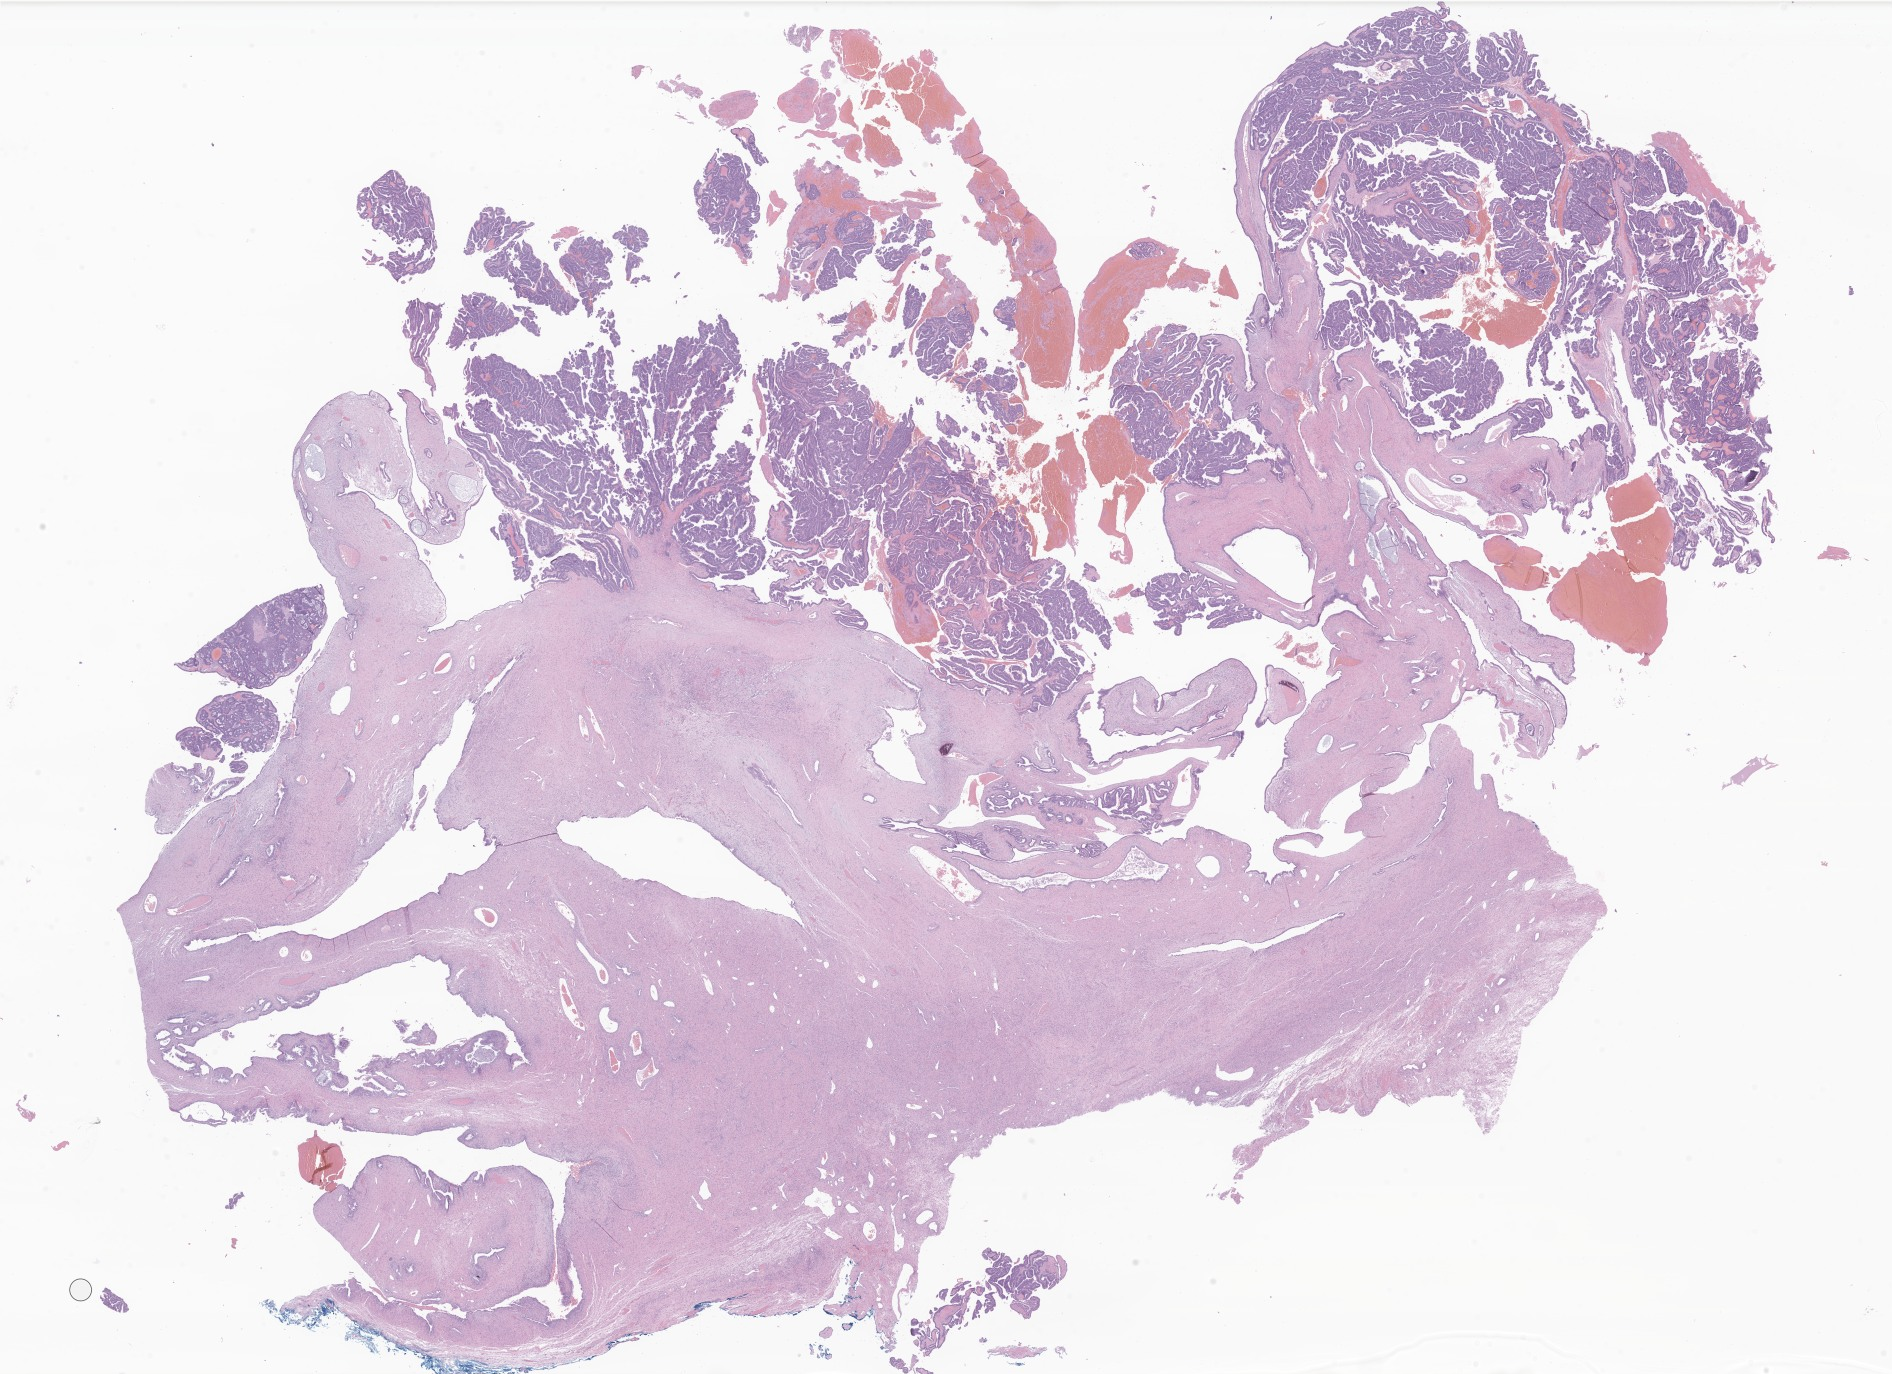
Hematoxylin and eosin (H&E) whole-slide image of tumor tissue from the ovary — a low-resolution overview of the entire scanned area, about 31.9 x 23.2 mm. Formalin-fixed, paraffin-embedded (FFPE) tissue. Patient female; age 164 months (13 years 8 months).
Diagnosis (ICD-O-3 morphology term): Endometrioid adenocarcinoma, NOS.